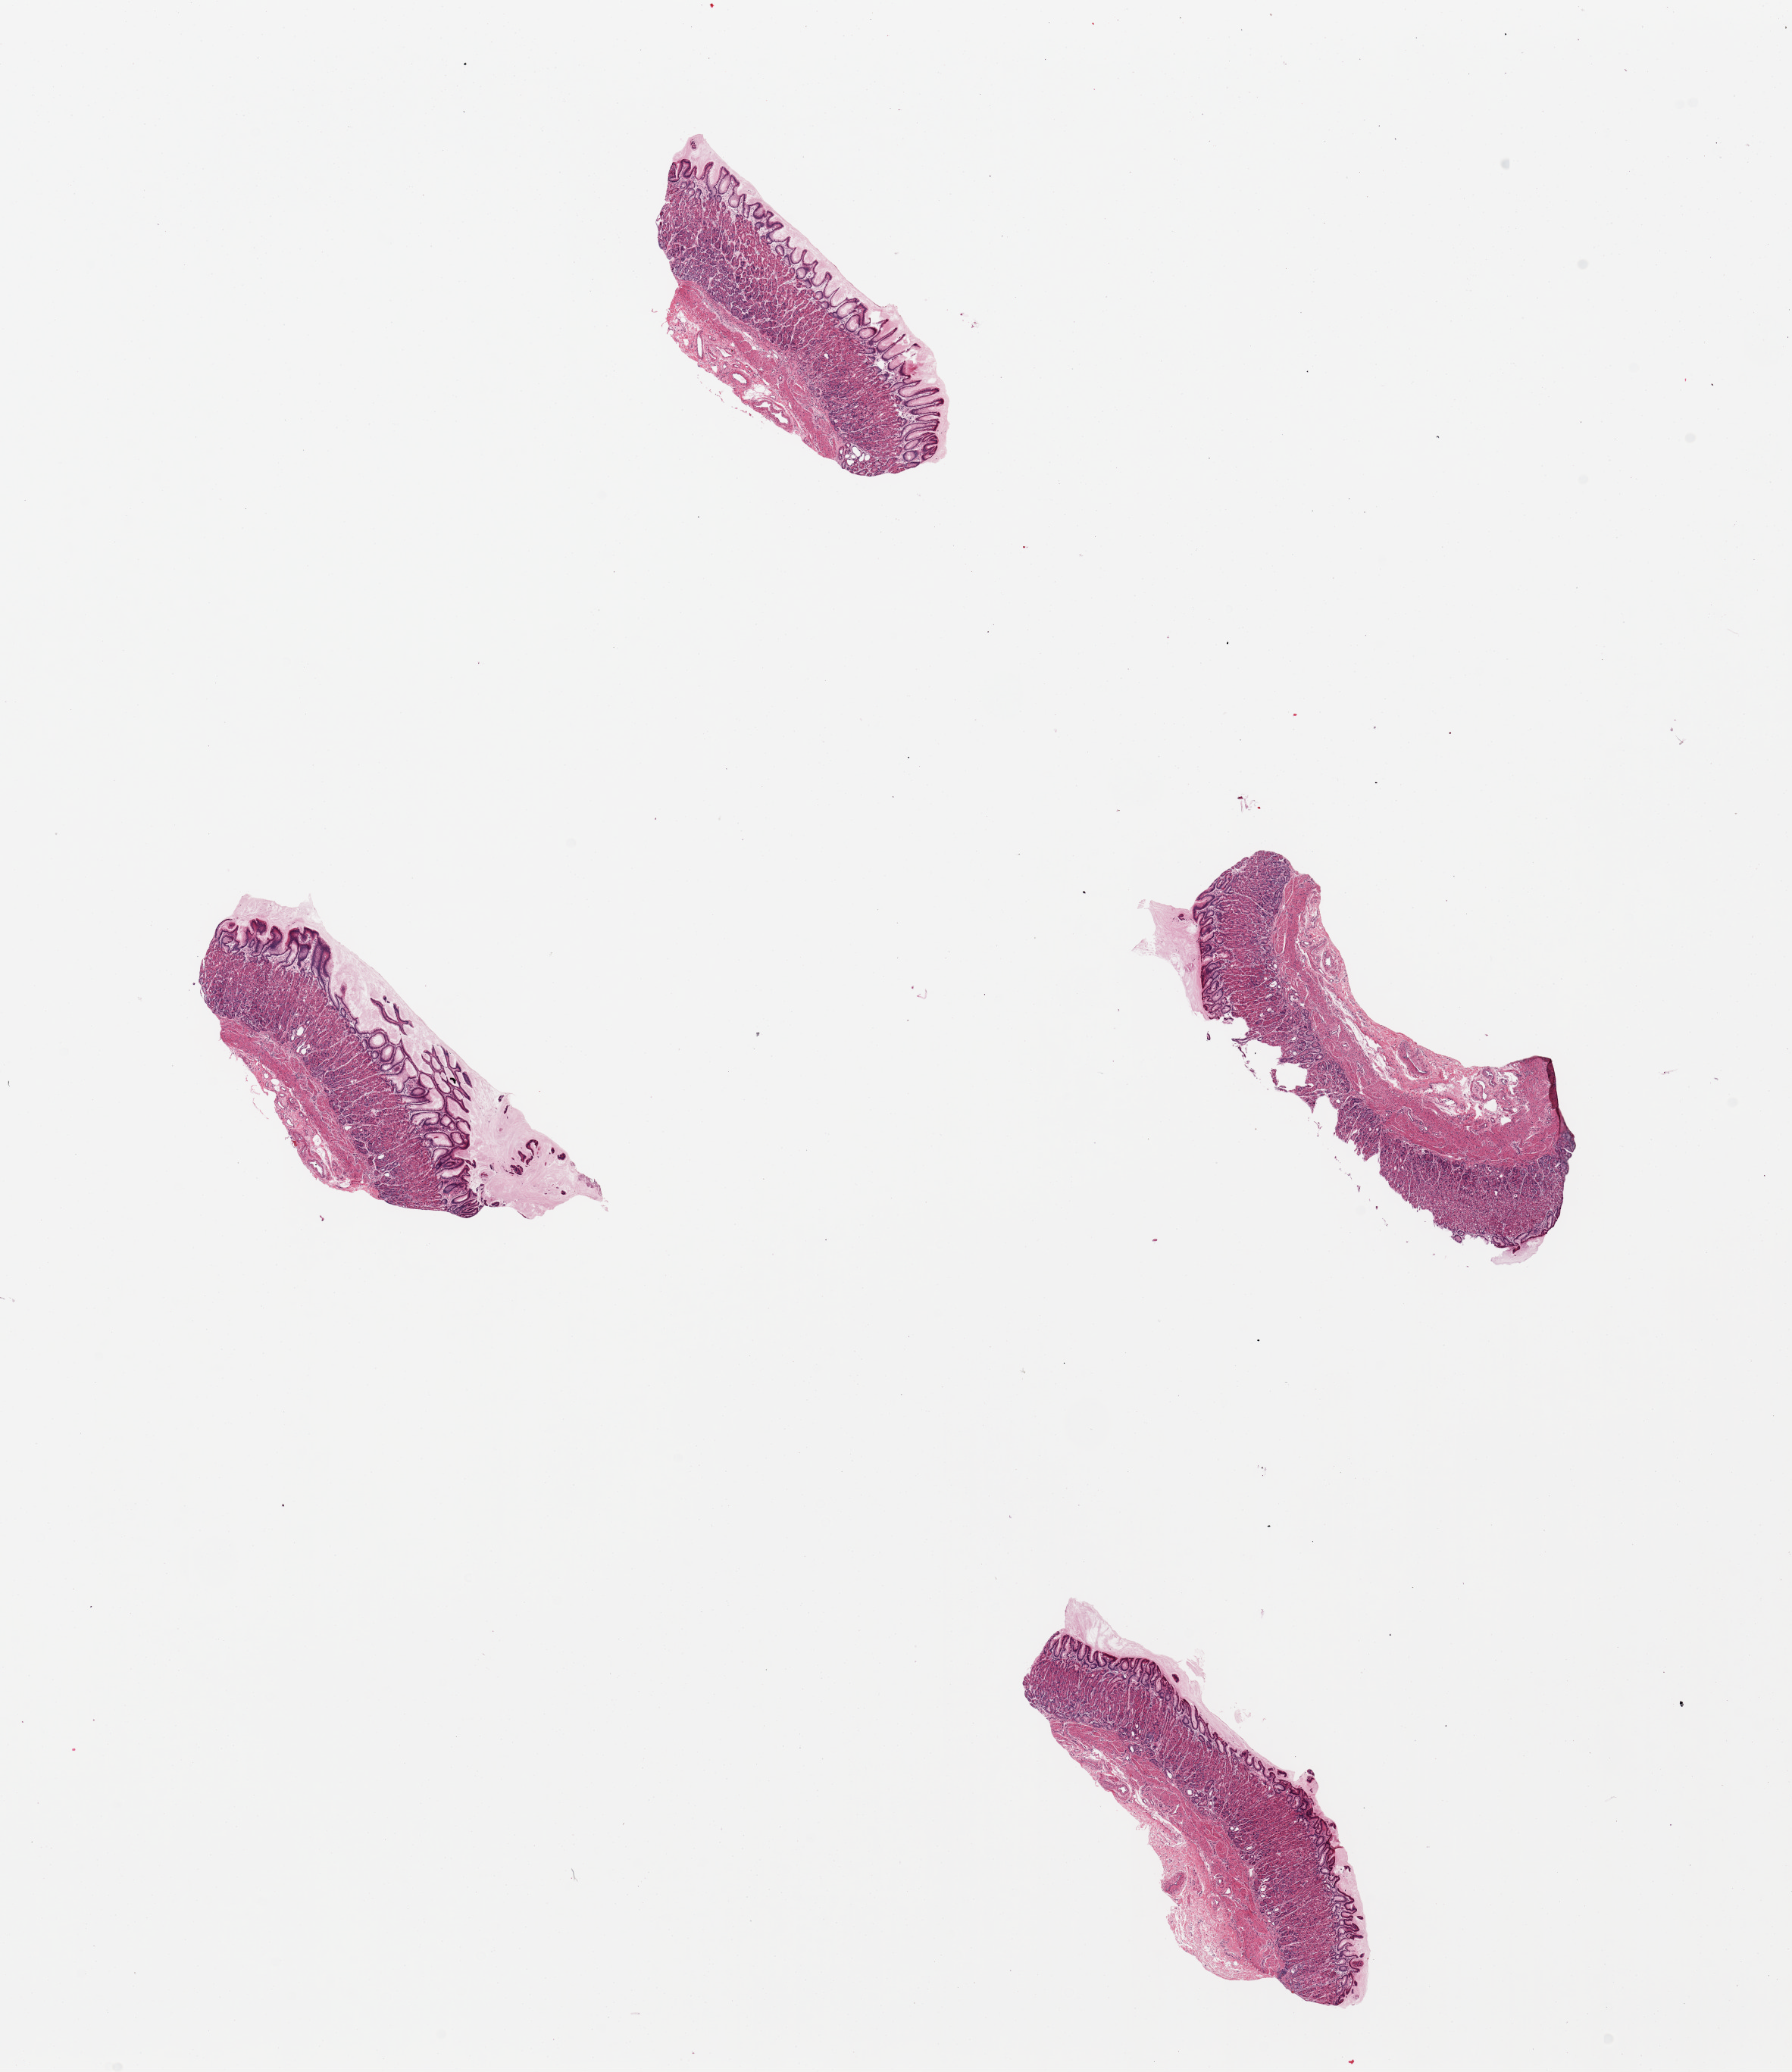
Digitized H&E-stained section, brightfield — low-resolution overview of the scanned area, about 18.7 x 21.6 mm. Donor: female.
Specimen: PAXgene-fixed paraffin-embedded (PFPE) section; section of gastroesophageal junction (target tissue); tissue donor sample.